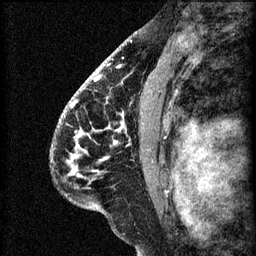
Breast MRI (dynamic contrast-enhanced), one sagittal slice; 3 images stored at this slice position (order not interpretable as contrast timing); 1.5 T; TE 4.2 ms, TR 8.2 ms; 2.2 mm slice thickness; 256 × 256 image matrix, field of view 180 × 180 mm. Female patient, age 41 years.
Structures marked on this image (semi-automatically segmented with operator editing):
- analysis volume of interest (the breast-tissue region the enhancement analysis was run in; not a lesion): bounding box (x1, y1, x2, y2) in pixels: (56, 104, 157, 207)
- tumour enhancement mask (voxels above the 70 % enhancement threshold inside the analysis volume of interest): (72, 106, 123, 177)